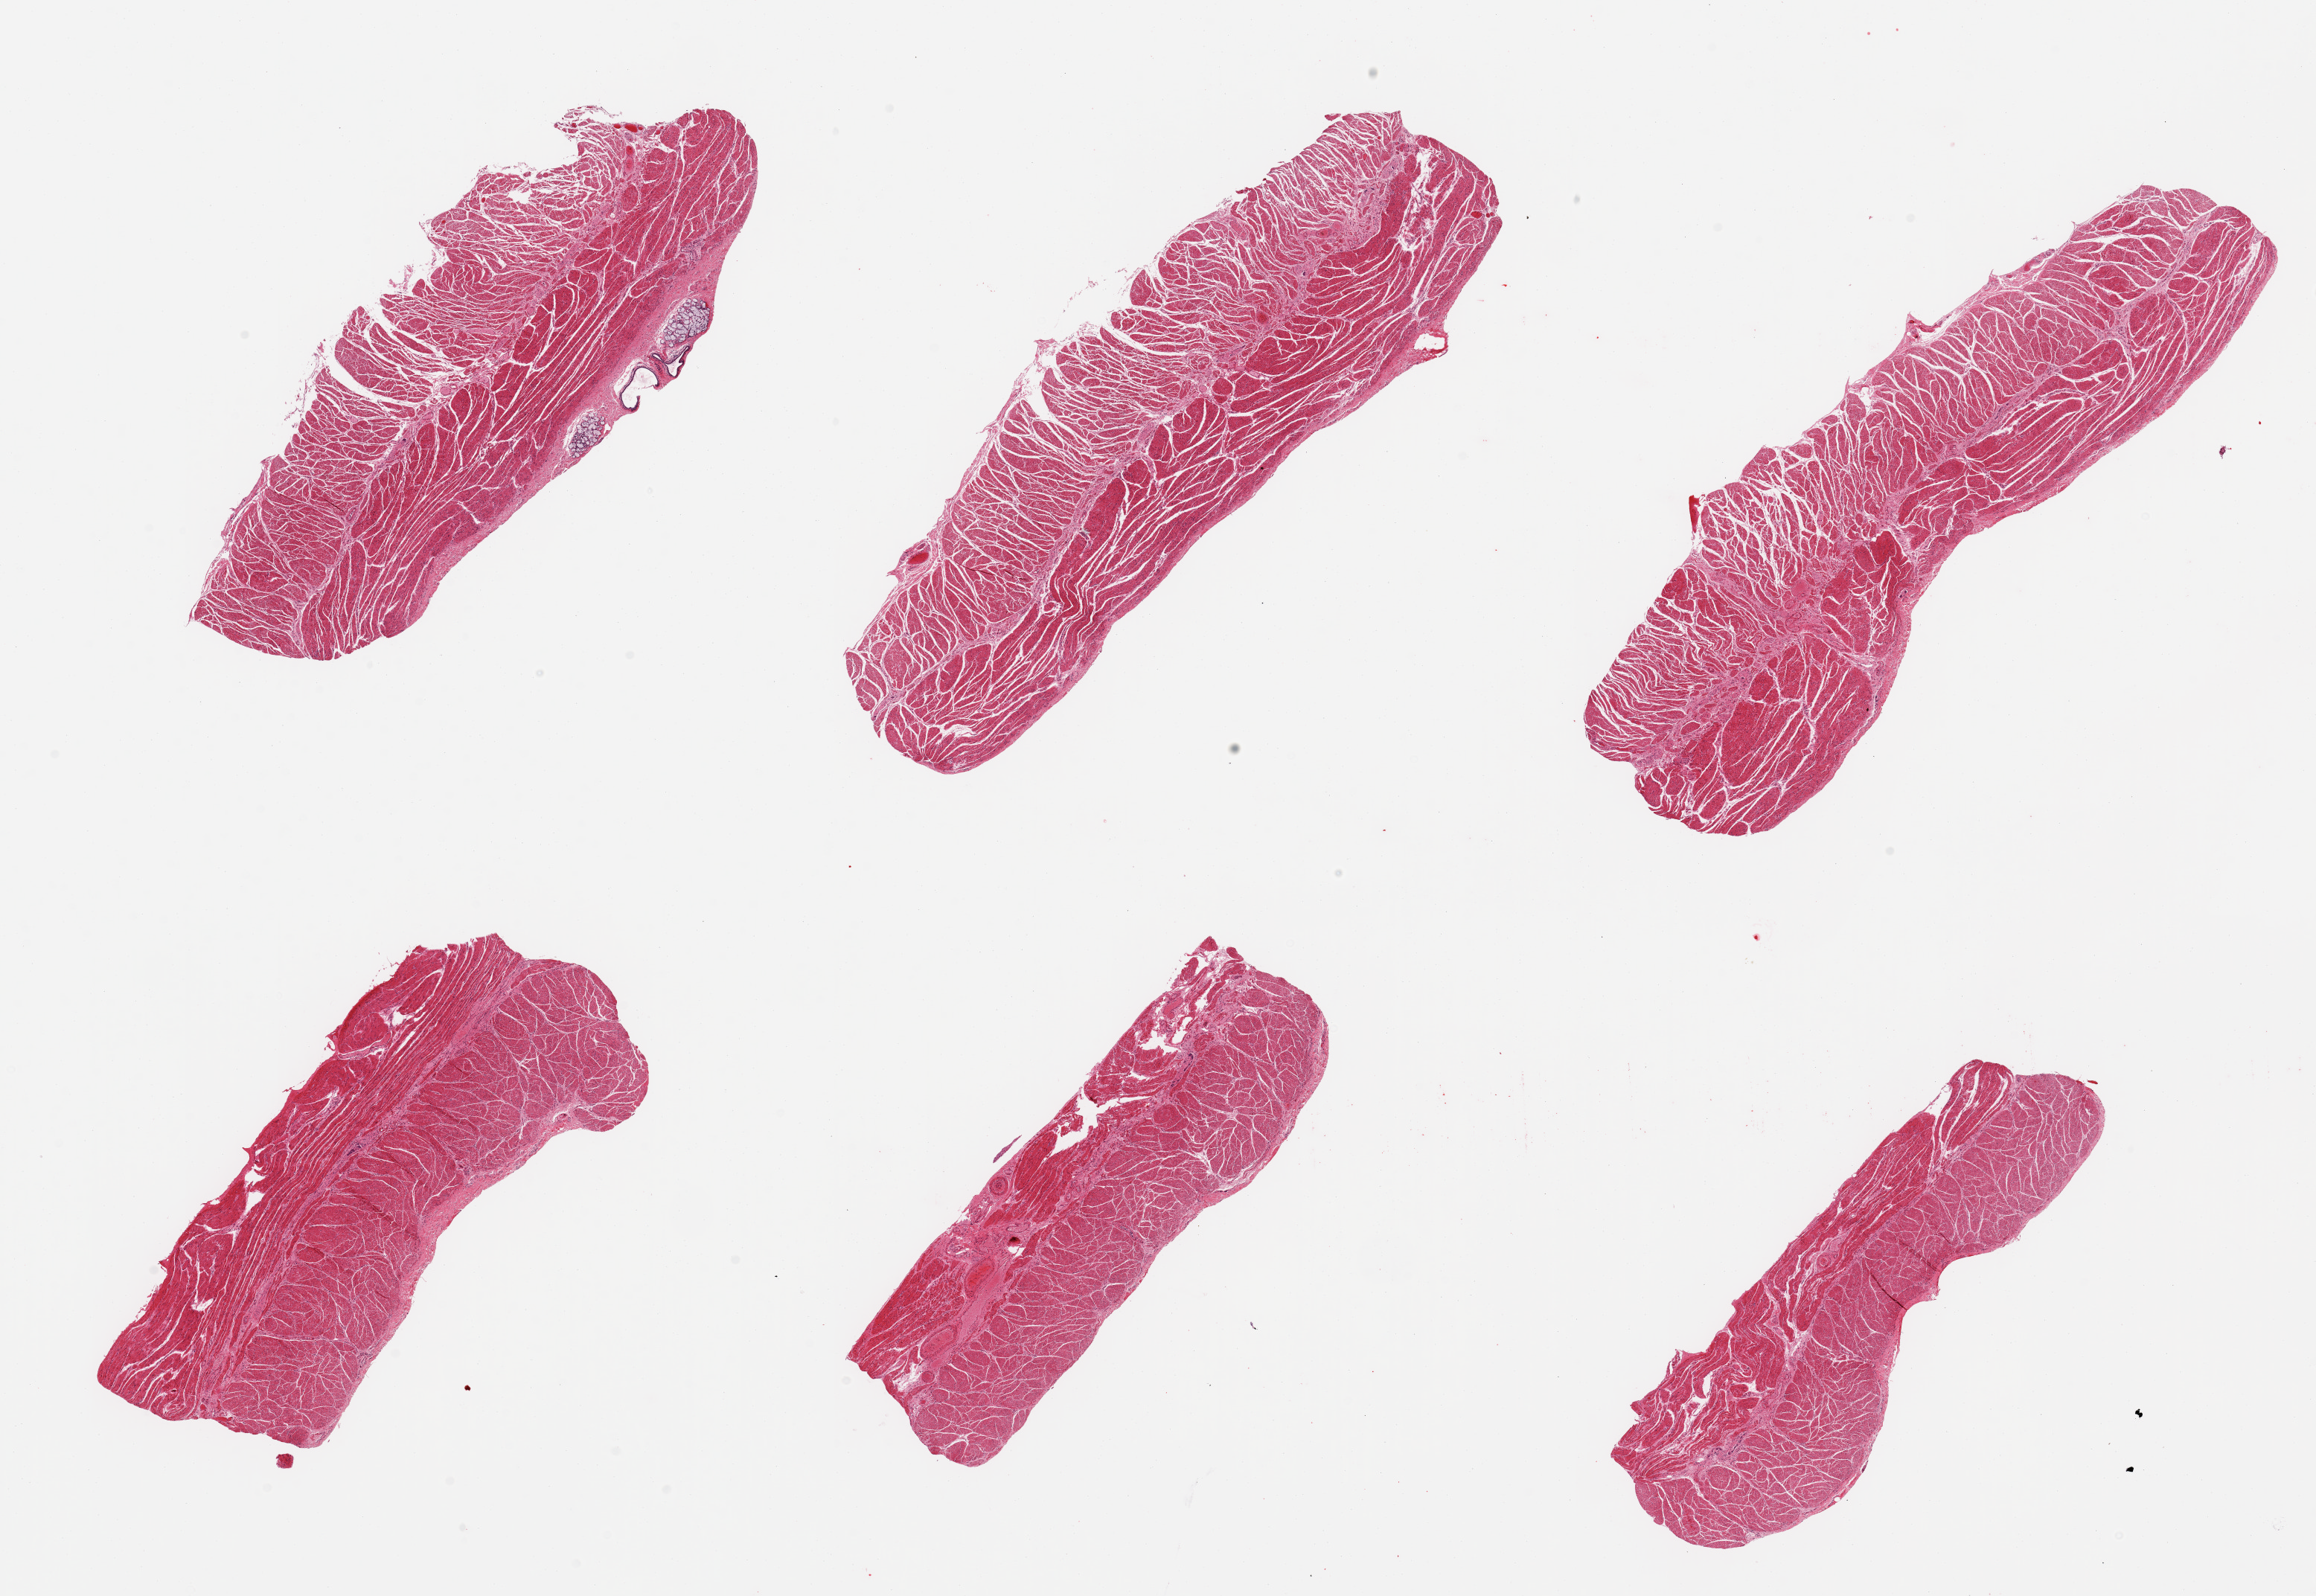
Hematoxylin and eosin (H&E) whole-slide image, whole scanned area (about 24.6 x 17.0 mm) shown as a low-resolution overview. PAXgene-fixed paraffin-embedded (PFPE) section. Sampled site (target tissue): esophageal muscle. Tissue donor sample. Donor sex: male.
Pathologist's review note for this sample: 6 pieces, confirmed target muscularis.